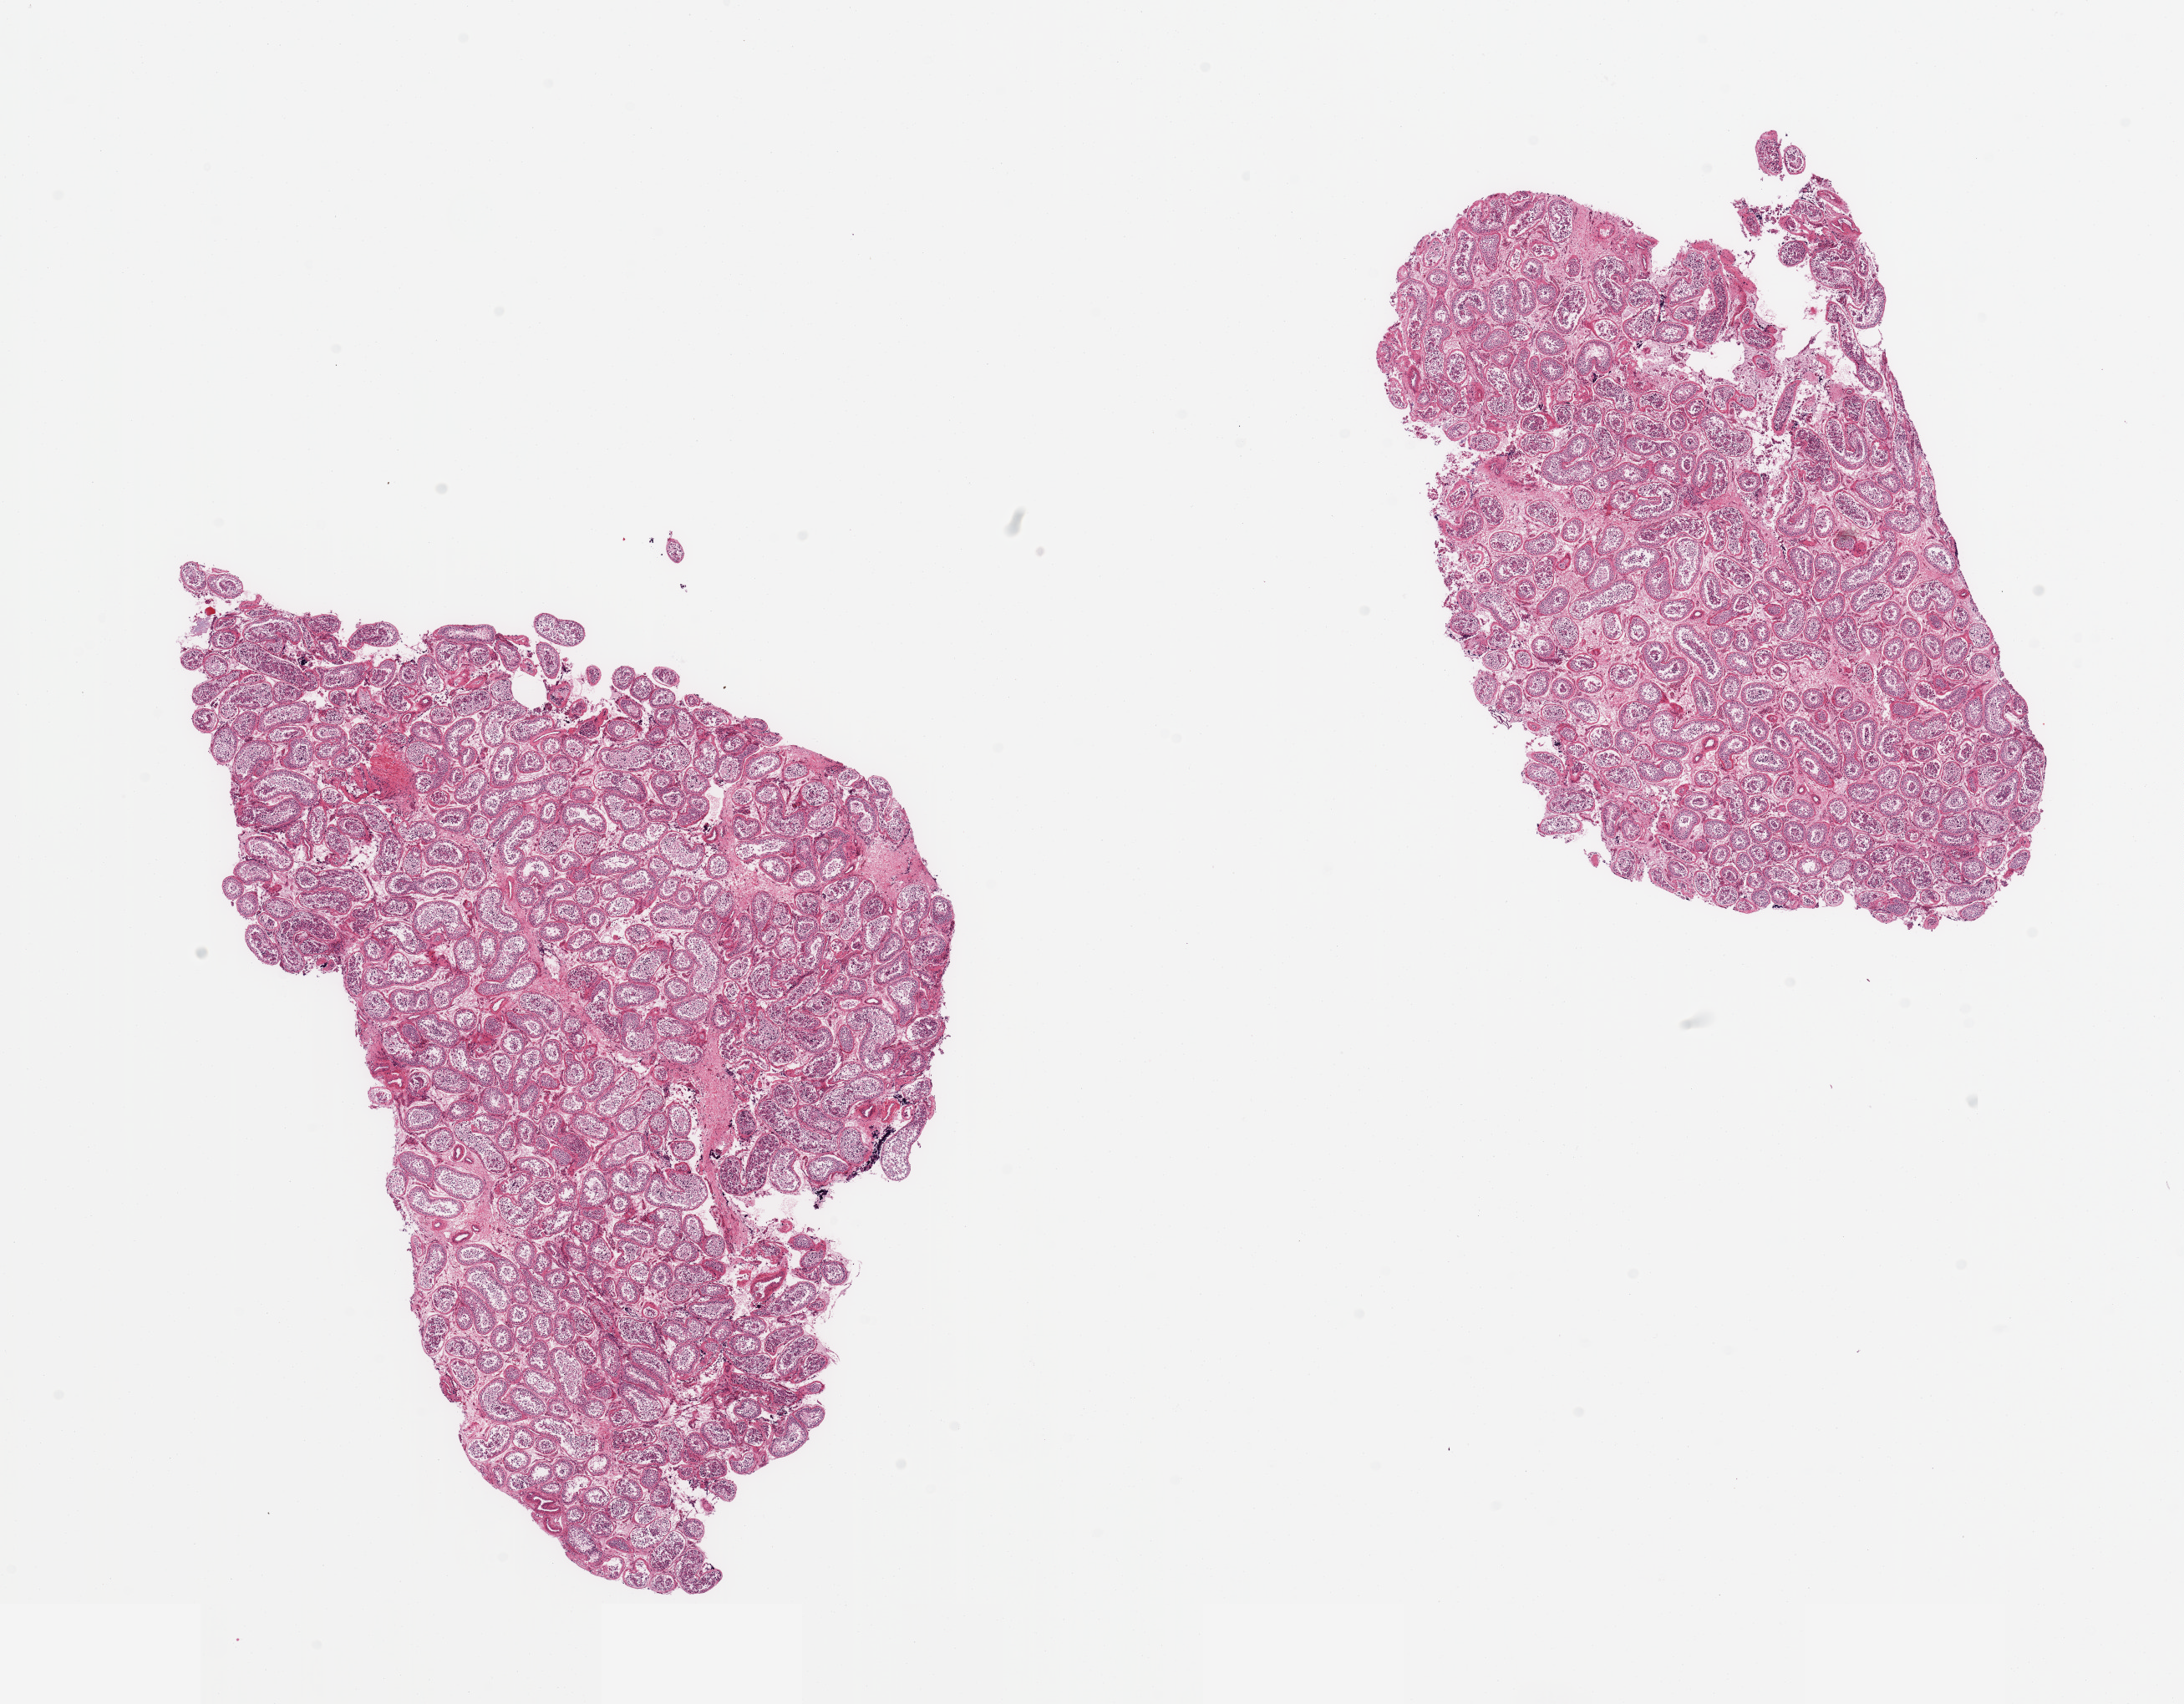
Hematoxylin and eosin (H&E) whole-slide image — shown as a low-resolution overview of the whole scanned area (about 20.7 x 16.1 mm), PAXgene-fixed, paraffin-embedded tissue, section of testis (target tissue), tissue donor sample. Donor: male.
Reviewer comment on this tissue sample: 2 pieces; spermatogenesis present.